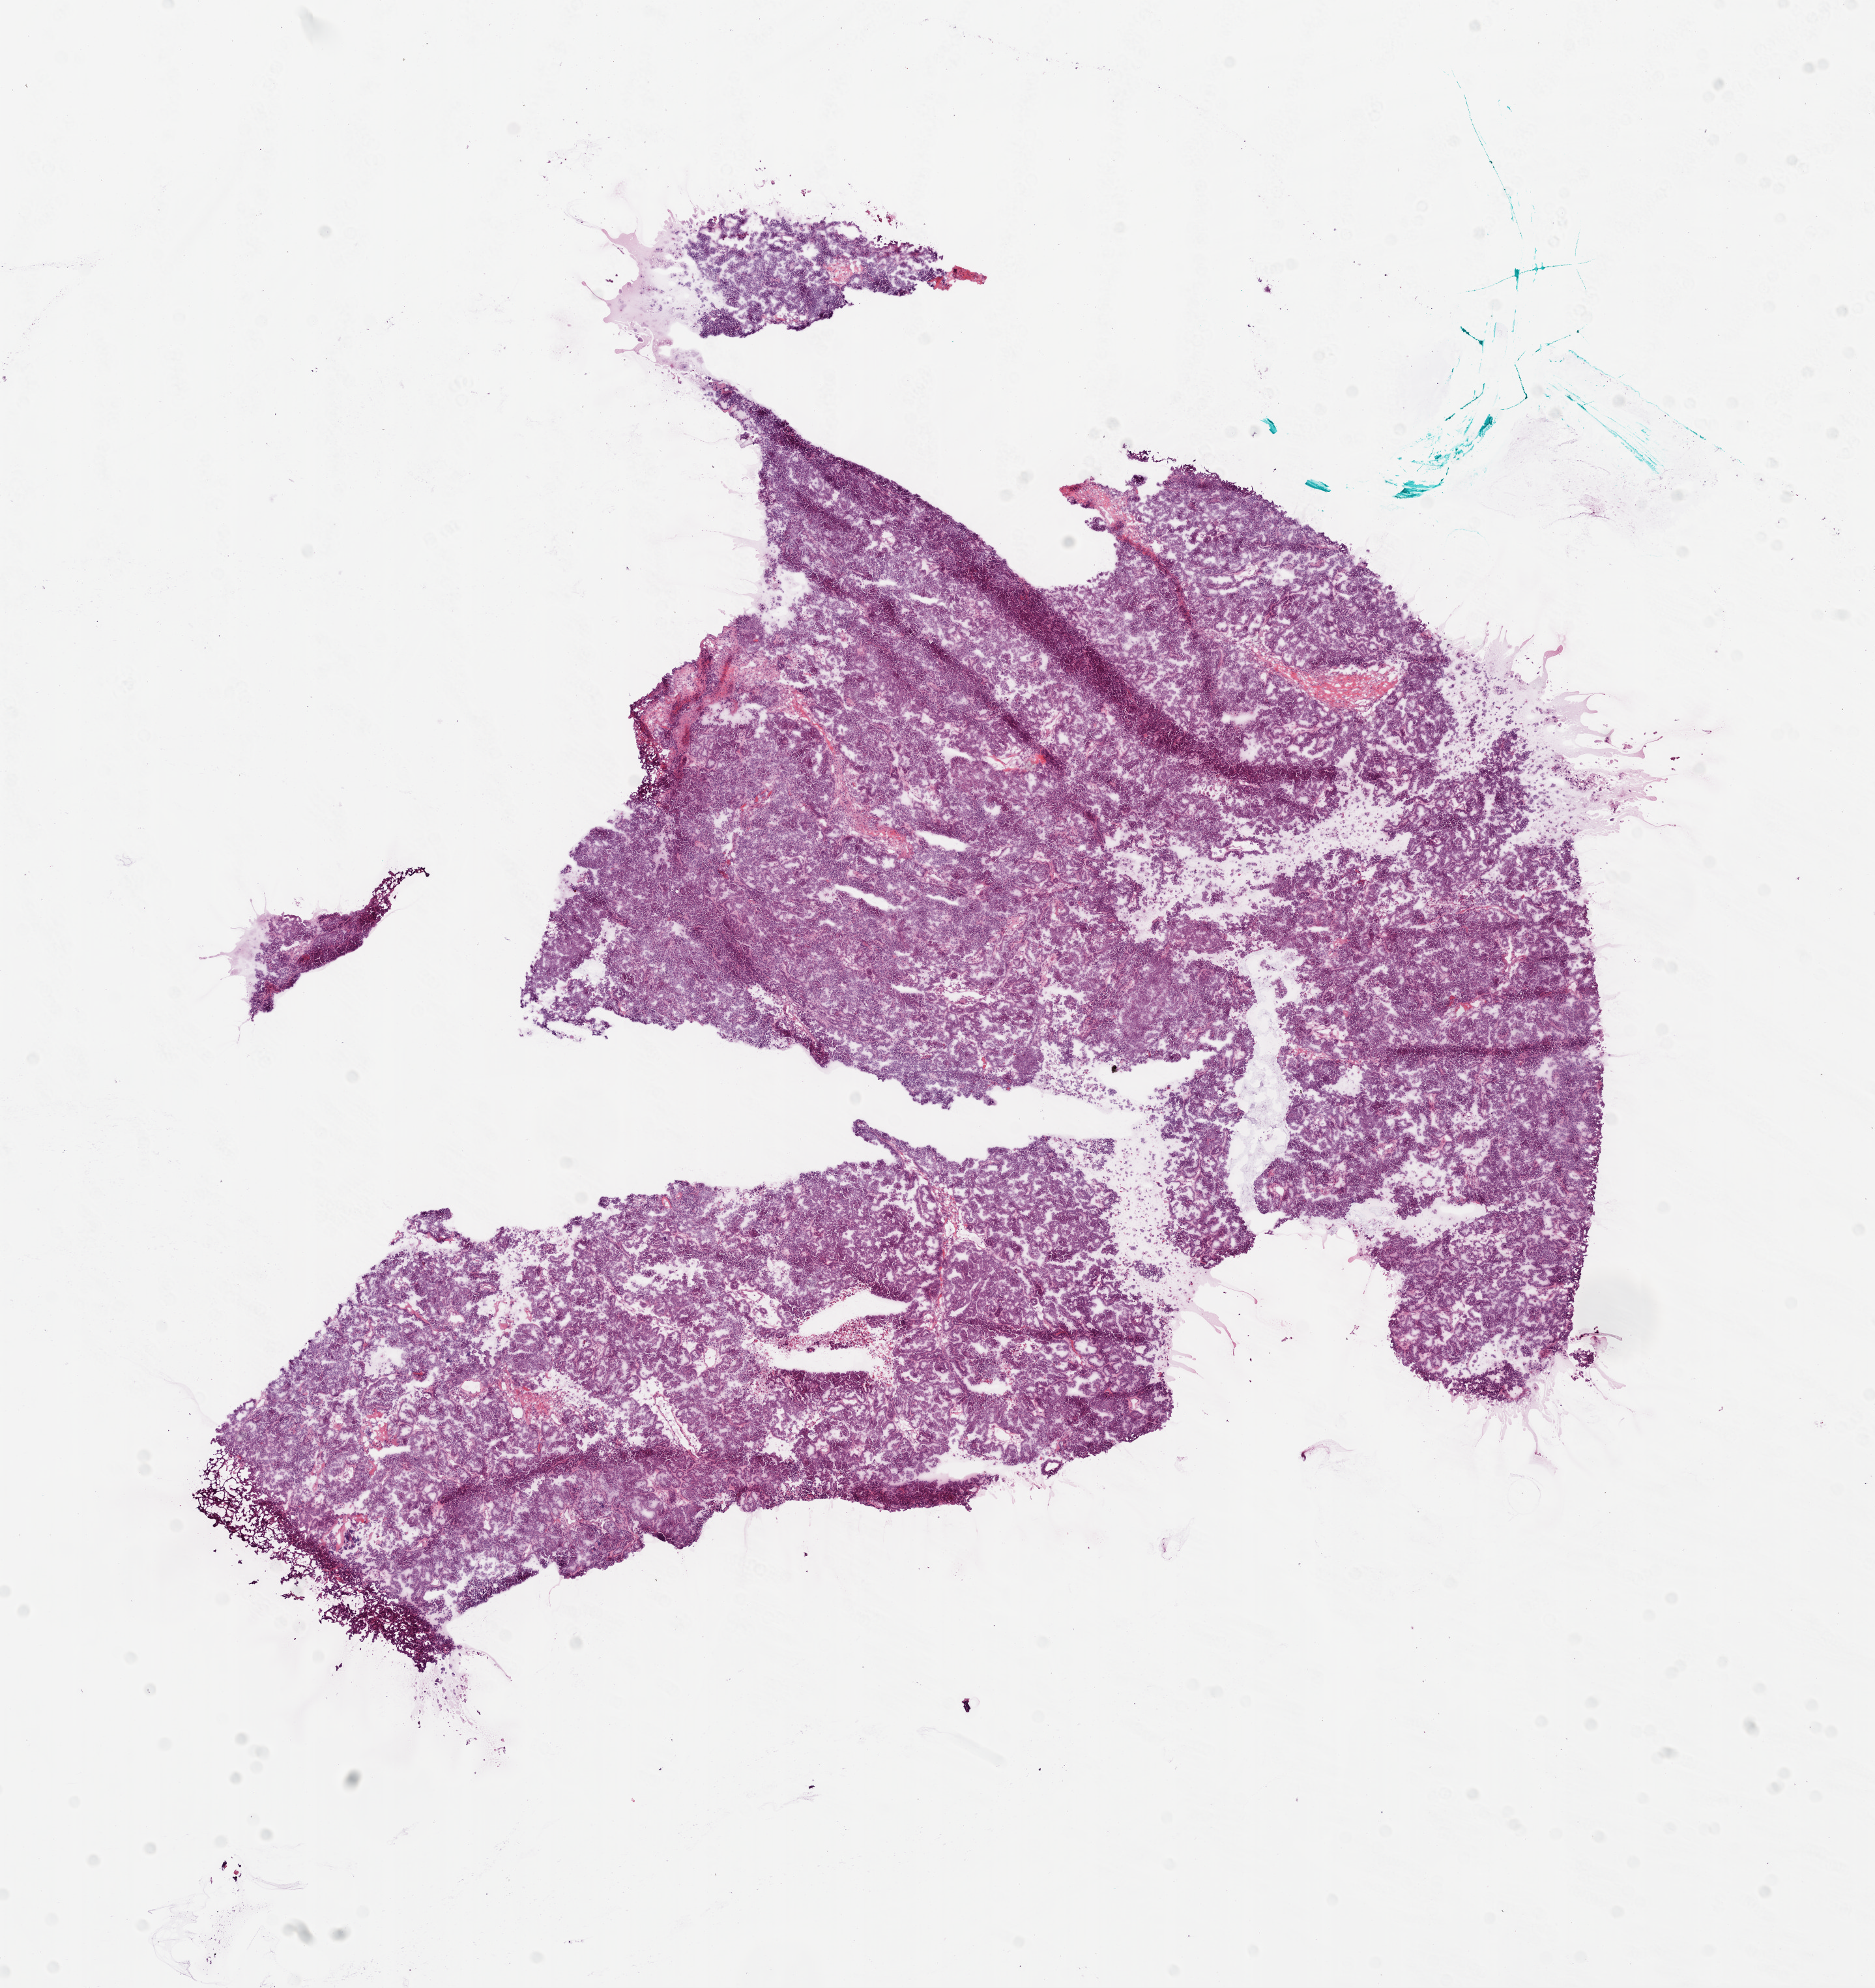
H&E whole-slide image, low-resolution overview of the scanned area, about 11.6 x 12.3 mm (from a 20x scan). Frozen section. Sample: primary tumour, ovary. Female, age 68 years at initial diagnosis. Histologic grade: G3 (poorly differentiated). Pathologist review of this section (percent, as recorded): tumour cells 95%, tumour nuclei 95%, normal cells 0%, stromal cells 5%, necrosis 0%.
• FIGO stage: IIIC
• laterality: bilateral
• diagnosis: Serous cystadenocarcinoma, NOS